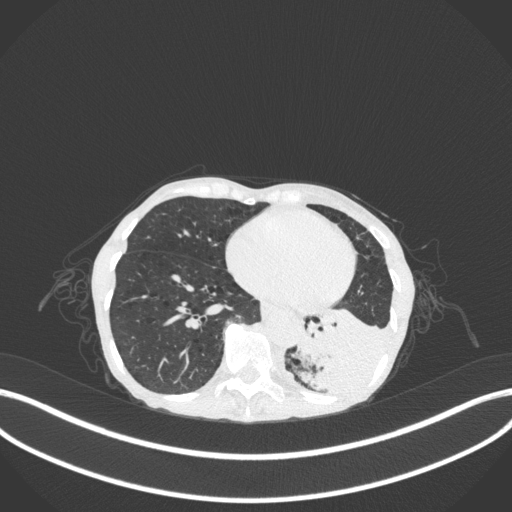
Chest CT, one axial slice. Slice 79 of 347 in the series (ordered by position). 120 kVp. Lung window (W 1500 / L -600 HU). 1 mm slice thickness. 512 × 512 image matrix. Female patient, age 70 years. Case-level facts recorded for this patient, not image findings: clinical TNM (as recorded): T3 N0 M0.
Outlined on this slice (rectangle marked by the reading radiologist):
- lung tumour (recorded histology: small cell carcinoma): bounding box (x1, y1, x2, y2) in pixels: (294, 295, 393, 402)